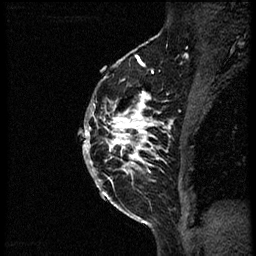
Breast MRI (dynamic contrast-enhanced), one sagittal slice. Position 40 of 56 along the scan axis. Dynamic contrast-enhanced study with each time point stored as its own series, time point 2 of 3 at this slice position (early post-contrast, ordered by acquisition time). 1.5 T. TE 4.2 ms, TR 21.3 ms. 2 mm slice thickness. 256 × 256 image matrix, field of view 200 × 200 mm. Patient: female, 41 years. Case-level facts recorded for this patient, not image findings: setting: breast cancer imaged before/during neoadjuvant chemotherapy; receptor status: HER2-positive.
Structures marked on this image (semi-automatically segmented with operator editing):
- analysis volume of interest (the breast-tissue region the enhancement analysis was run in; not a lesion): bounding box <88,73,172,205> (left, top, right, bottom; pixels)
- tumour enhancement mask (voxels above the 100 % enhancement threshold inside the analysis volume of interest): <88,92,169,181>